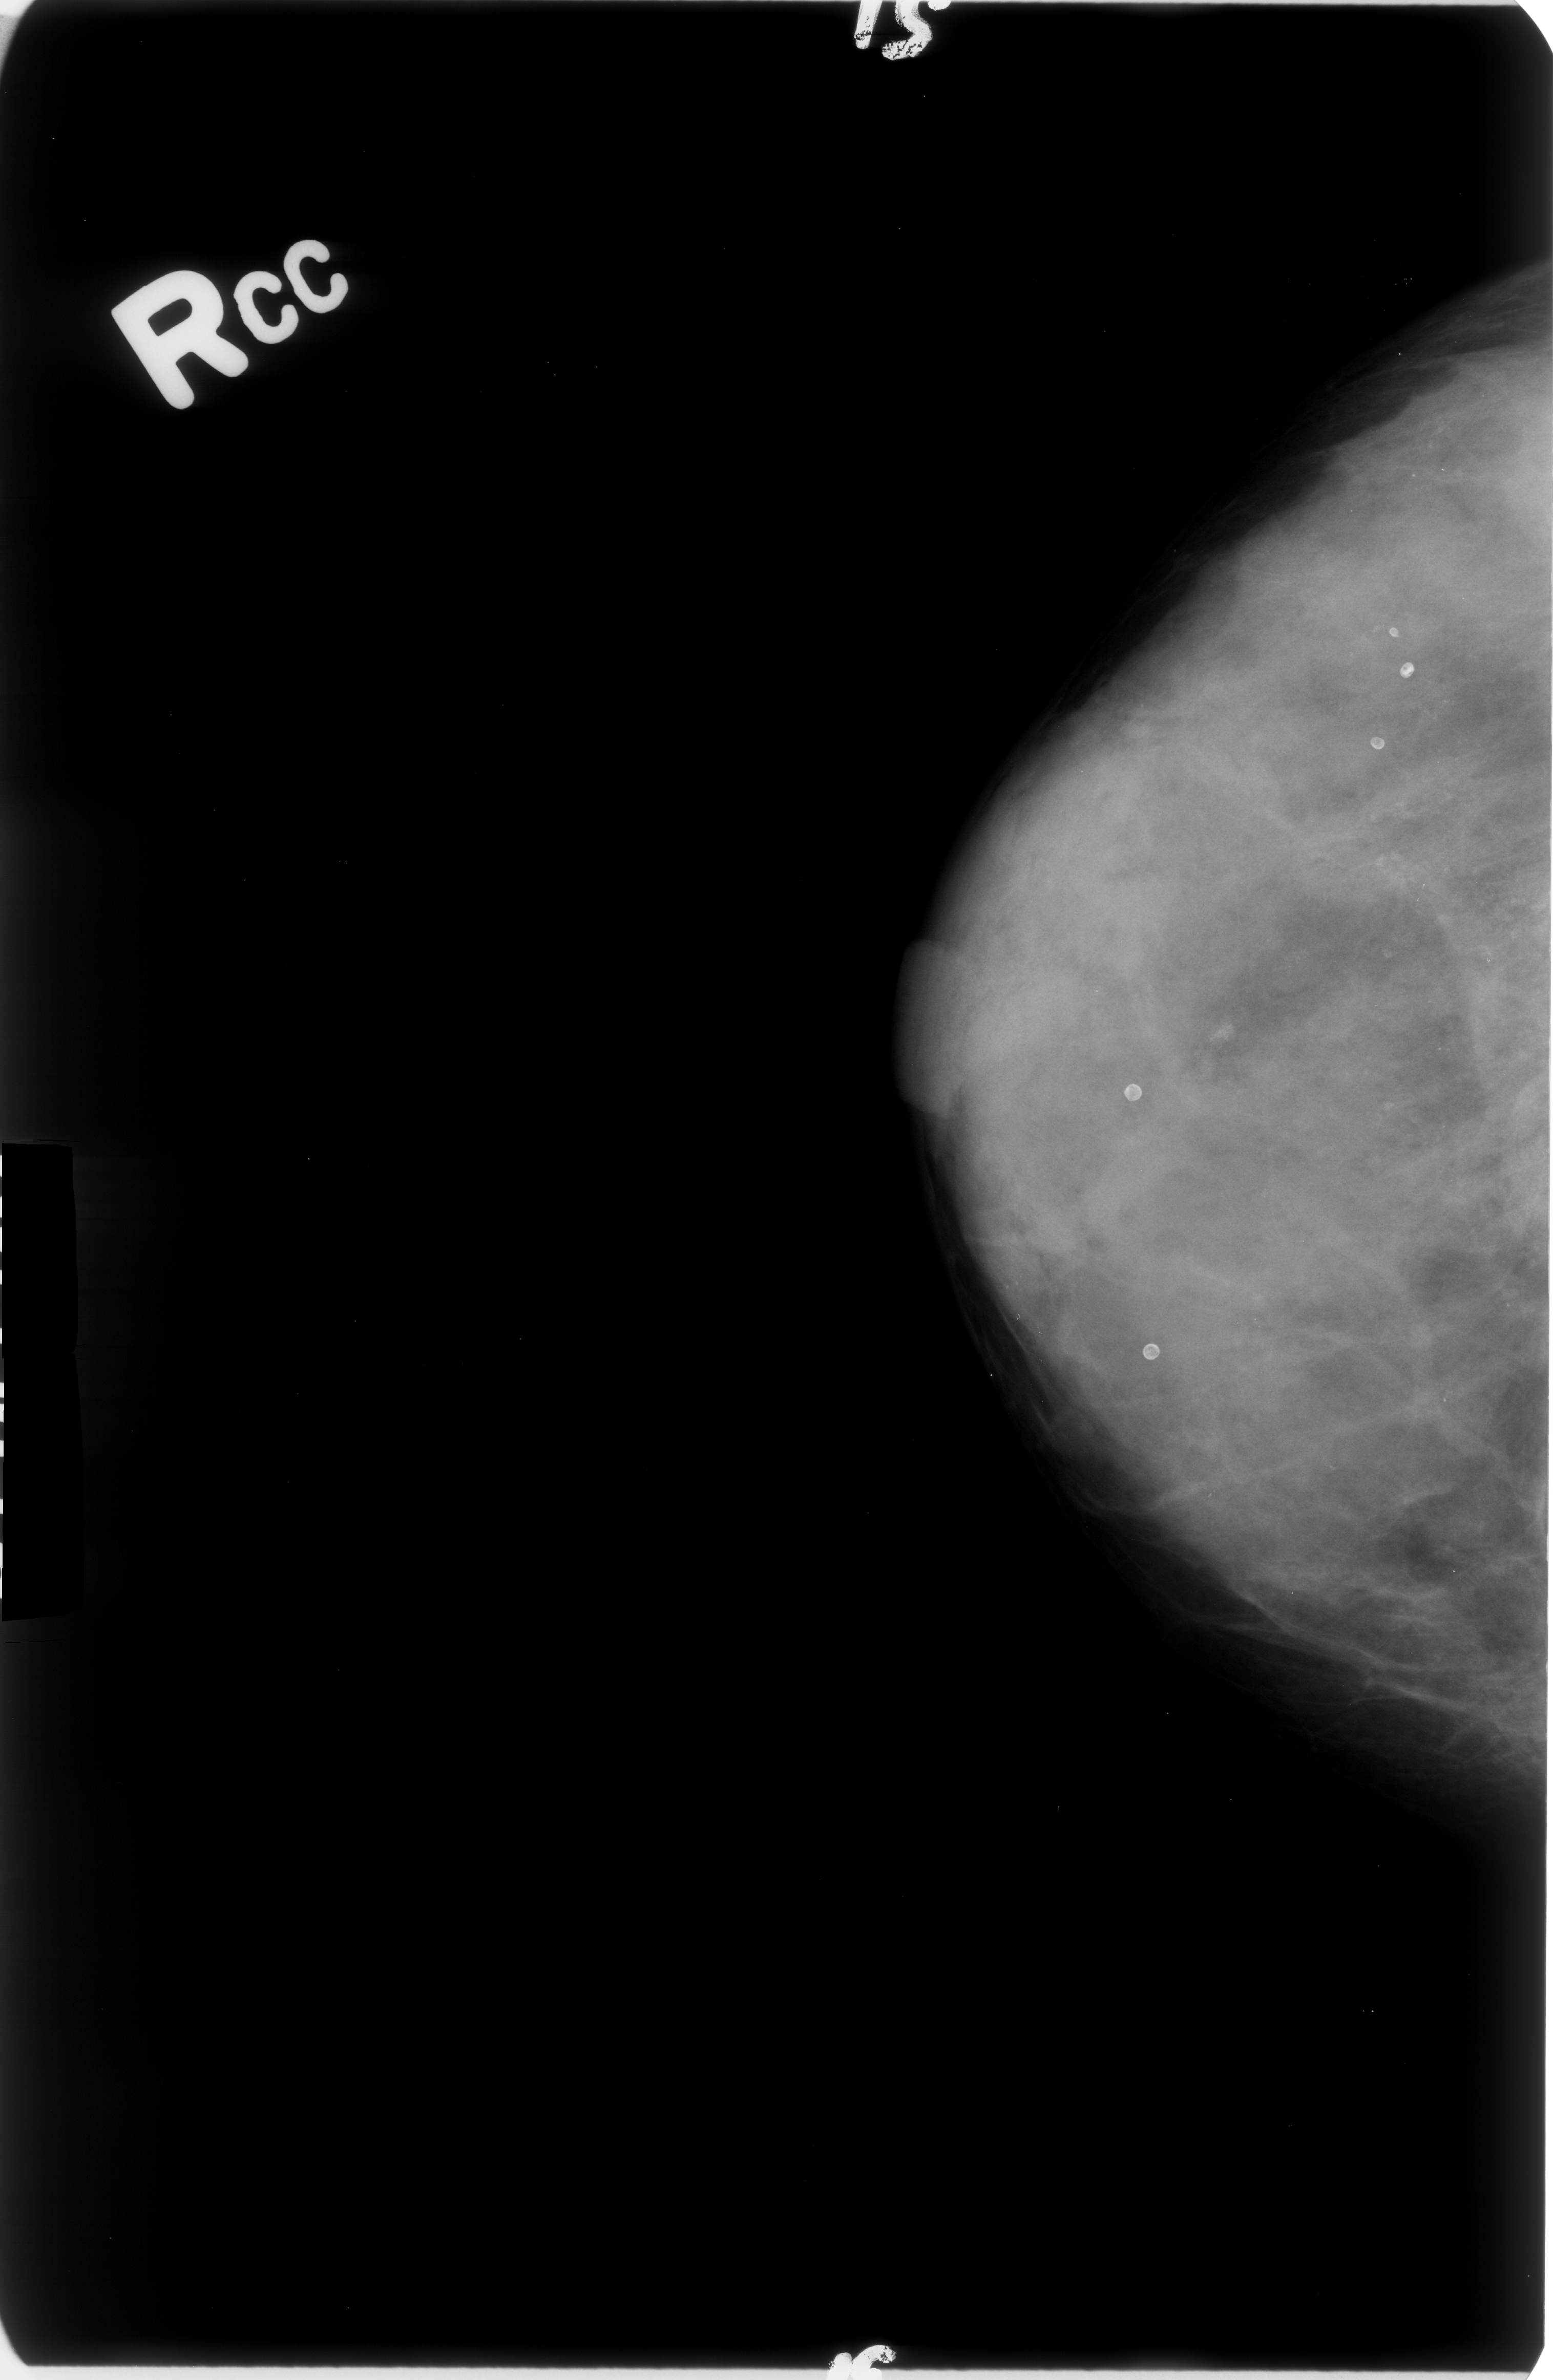
Mammogram (digitized film); right breast; craniocaudal (CC) view; BI-RADS breast density category 4 (scale 1–4); 1553 × 2380 image matrix.
Expert-marked regions of interest on this image (one box per marked abnormality):
- Finding 1 of 2: calcifications, morphology punctate / amorphous, distribution clustered; BI-RADS assessment category 4; subtlety rating 4 on a 1 (subtle) to 5 (obvious) scale; pathology (as recorded): benign: bounding box [x1, y1, x2, y2] px = [1167, 979, 1275, 1095]
- Finding 2 of 2: calcifications, morphology punctate / amorphous, distribution regional; BI-RADS assessment category 4; pathology result (as recorded, not read from the image): benign: [1303, 622, 1550, 1250]